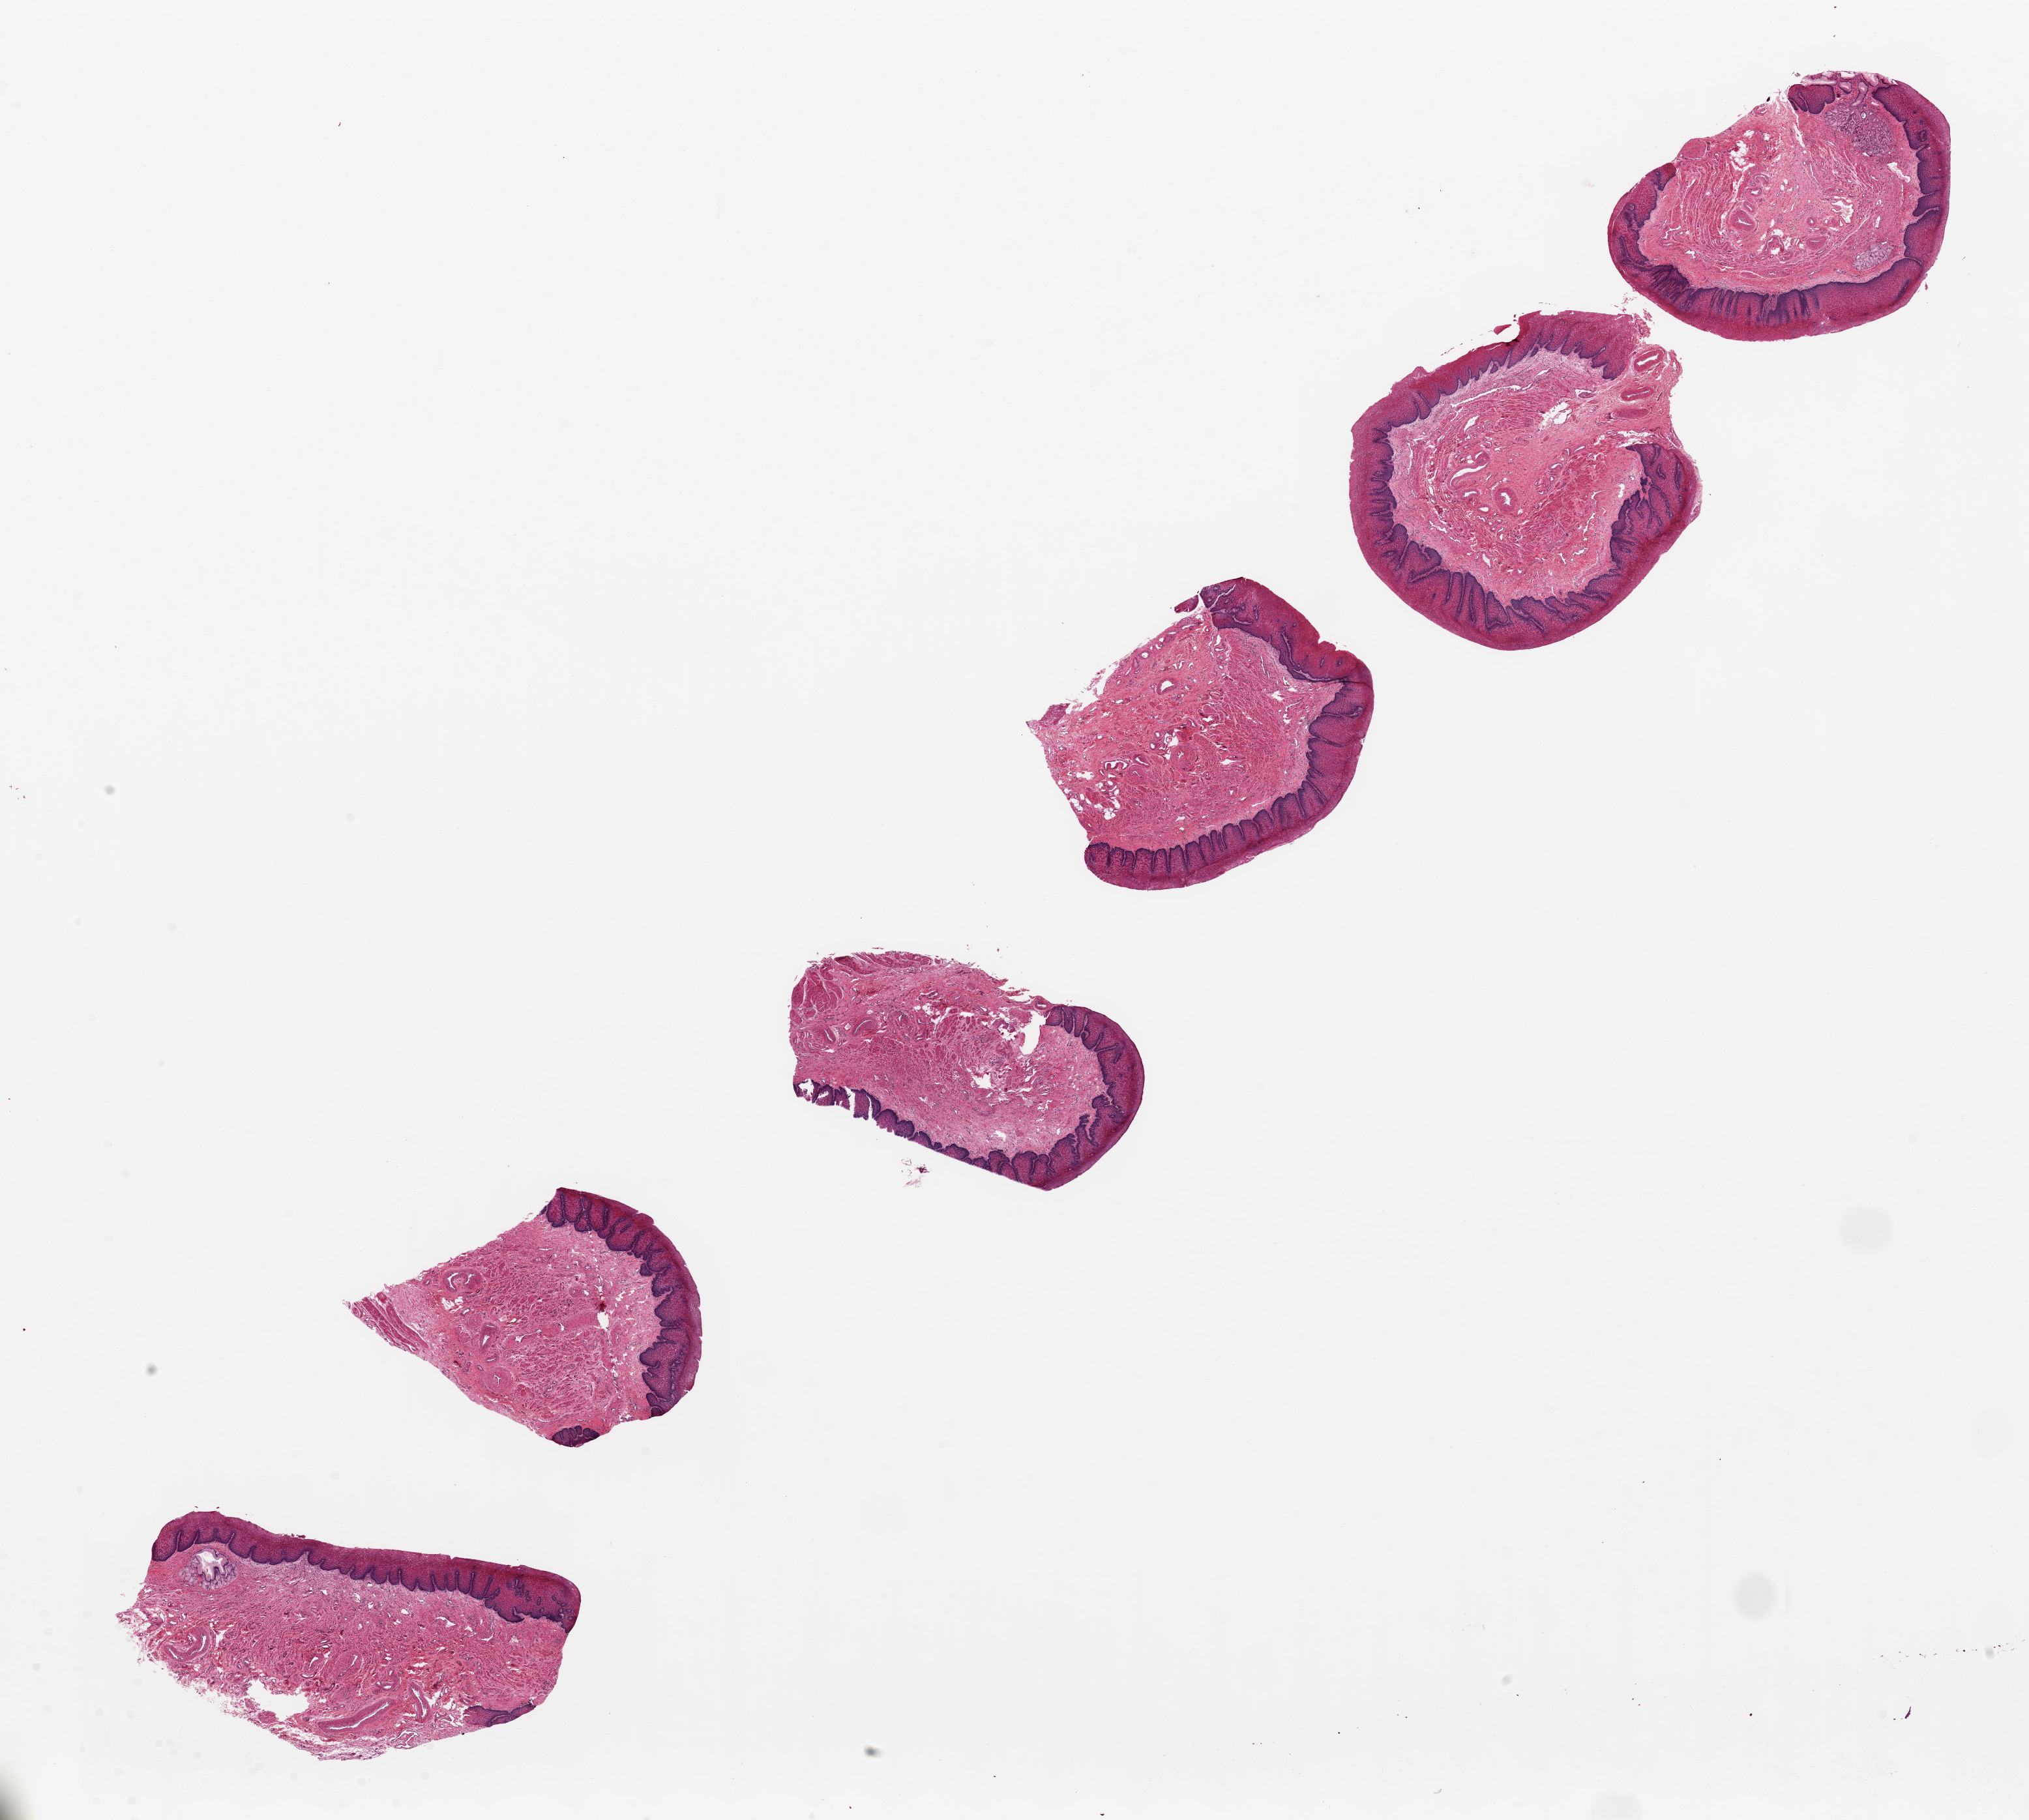
Whole-slide image, H&E stain, brightfield, whole scanned area (about 24.6 x 22.1 mm) shown as a low-resolution overview; PAXgene-fixed paraffin-embedded (PFPE) section; target tissue: esophageal mucous membrane; donor tissue sample. Female donor.
* reviewer comment on this tissue sample: 6 pieces ~4x4mm. Squamous mucosa is 10-15% of thickness